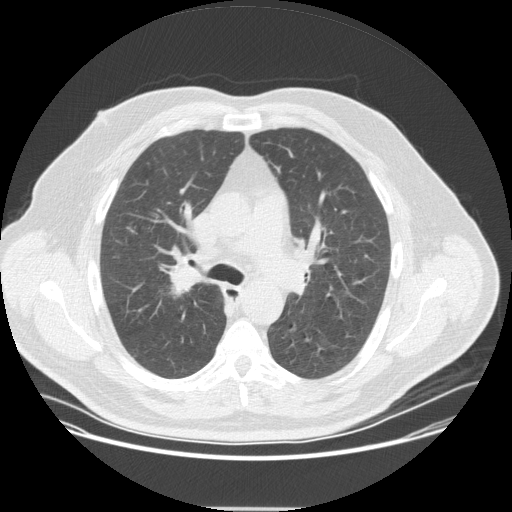
Chest CT (low-dose screening protocol), one axial image. Second annual screen. Lung window (W 1500 / L -600 HU). 2.5 mm slice thickness. Standard (soft-tissue) reconstruction kernel (STANDARD). 120 kVp. Male, age 57 years at enrolment. Current smoker at enrolment.
- Lesion marked by an expert reader, bounding box <152,253,210,307> (left, top, right, bottom; pixels).
- Screening reader's record for this exam (one nodule recorded; not confirmed to be the boxed lesion): non-calcified nodule or mass ≥4 mm, right upper lobe, 20 × 16 mm, spiculated (stellate) margins, soft tissue attenuation, pre-existing on the prior screen: no.
- Later outcome: lung cancer diagnosed 35 days after this screen — non-small cell carcinoma, right upper lobe, poorly differentiated (G3), stage IIA (AJCC 6th edition), 25 mm at pathology.